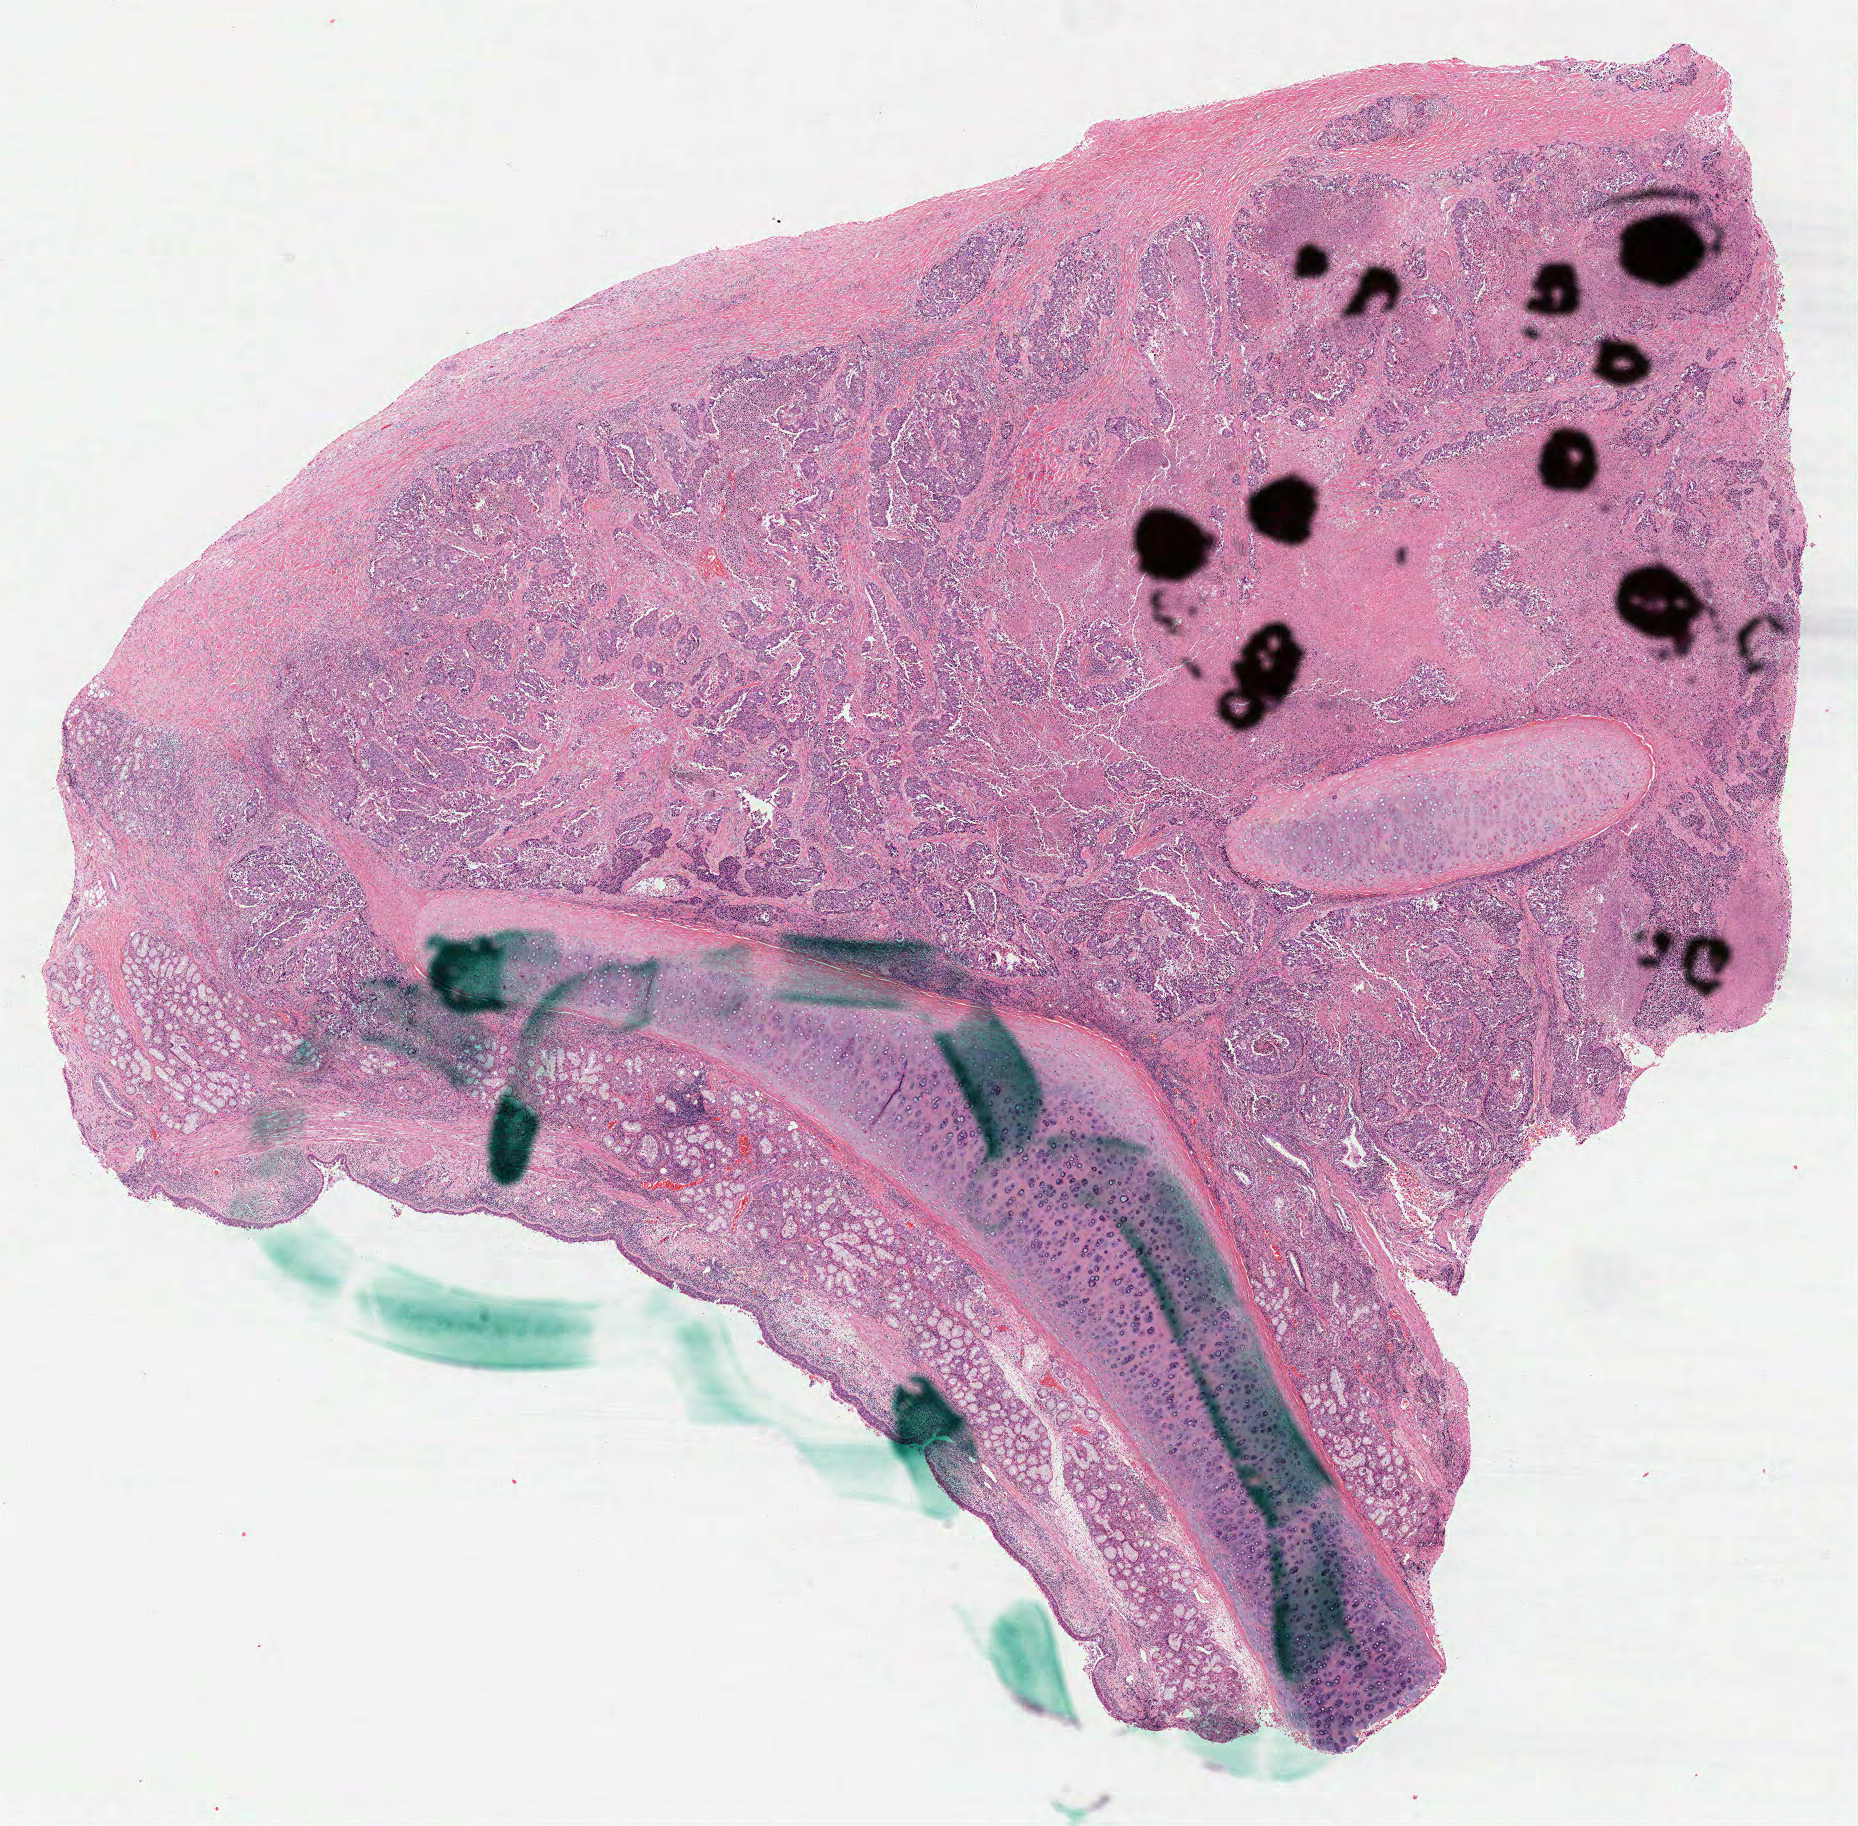
H&E whole-slide image, shown as a low-resolution overview of the whole scanned area (about 15.0 x 14.7 mm), formalin-fixed paraffin-embedded (FFPE) diagnostic section, sample: primary tumour, lung. Male, age 50 years at initial diagnosis.
* diagnosis: Squamous cell carcinoma, NOS (upper lobe, lung)
* AJCC pathologic stage: IIA (7th edition)
* TNM: T2a N1 M0